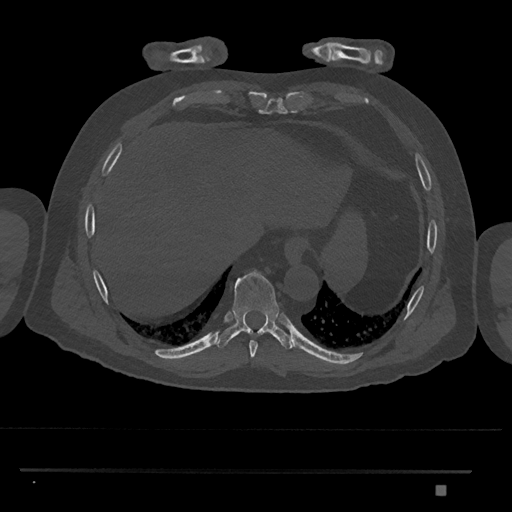
CT including the spine, one axial slice; slice 1072 of 1134 in the series (ordered by position); 120 kVp; bone window (W 1800 / L 400 HU); 512 × 512 image matrix, field of view 429 × 429 mm. Patient: male, 65 years. From the clinical record (not read from this slice): primary cancer: prostate.
Outlined on this slice (semi-automatic segmentation, software-assisted and operator-edited):
- T8 vertebra: bounding box <249,340,258,357> (left, top, right, bottom; pixels)
- T9 vertebra: <215,269,293,349>